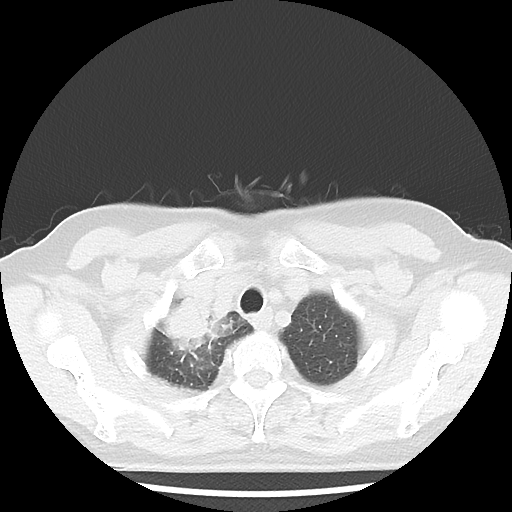
Chest CT, one axial slice; lung window (W 1500 / L -600 HU); 5 mm slice thickness; 512 × 512 image matrix, field of view 316 × 316 mm. Female patient, age 62 years. From the clinical record (not read from this slice): clinical TNM (as recorded): T3 N0 M0; histopathological grade: G3.
Outlined on this slice (rectangle marked by the reading radiologist):
- lung tumour (recorded histology: small cell carcinoma): bounding box <164,284,244,365> (left, top, right, bottom; pixels)